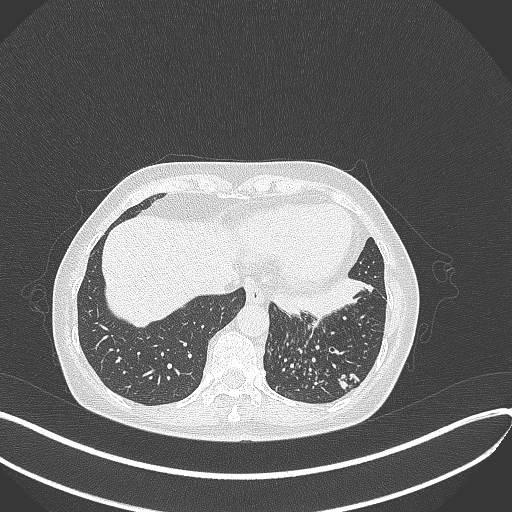
Chest CT, one axial slice; slice 100 of 429 in the series (ordered by position); reconstruction kernel B70f; 100 kVp; lung window (W 1500 / L -600 HU); 1 mm slice thickness; 512 × 512 image matrix, field of view 400 × 400 mm. Female patient, age 63 years. From the clinical record (not read from this slice): clinical TNM (as recorded): T1b N0 M0; histopathological grade: G2-3.
Outlined on this slice (rectangle marked by the reading radiologist):
- lung tumour (recorded histology: adenocarcinoma): bounding box [x1, y1, x2, y2] px = [277, 271, 372, 319]